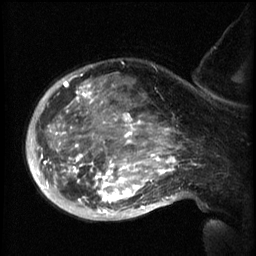
Breast MRI (dynamic contrast-enhanced), one sagittal slice. Position 44 of 60 along the scan axis. 3 images stored at this slice position (order not interpretable as contrast timing). 1.5 T. TE 4.2 ms, TR 8.2 ms. 2.3 mm slice thickness. 256 × 256 image matrix, field of view 200 × 200 mm. Female patient, age 50 years.
Outlined on this slice (semi-automatically segmented with operator editing):
- analysis volume of interest (the breast-tissue region the enhancement analysis was run in; not a lesion): bounding box [x1, y1, x2, y2] px = [50, 64, 169, 217]
- tumour enhancement mask (voxels above the 70 % enhancement threshold inside the analysis volume of interest): [50, 74, 169, 213]